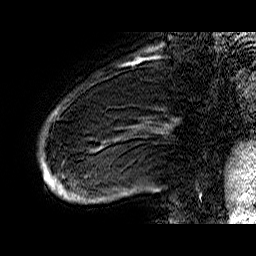
Breast MRI (dynamic contrast-enhanced), one sagittal slice; slice 9 of 60 in the series (ordered by position); dynamic contrast-enhanced series, time point 2 of 6 at this slice position (early post-contrast); 1.5 T; TE 6.4 ms, TR 32.9 ms; 4 mm slice thickness; 256 × 256 image matrix, field of view 200 × 200 mm. Female patient. From the clinical record (not read from this slice): setting: breast cancer imaged before/during neoadjuvant chemotherapy; receptor status: HR-positive, HER2-negative.
Annotated regions visible in this slice (semi-automatic segmentation, software-assisted and operator-edited):
- analysis volume of interest (the breast-tissue region the enhancement analysis was run in; not a lesion): bounding box <41,83,176,205> (left, top, right, bottom; pixels)
- tumour enhancement mask (voxels above the 100 % enhancement threshold inside the analysis volume of interest): <42,113,100,200>